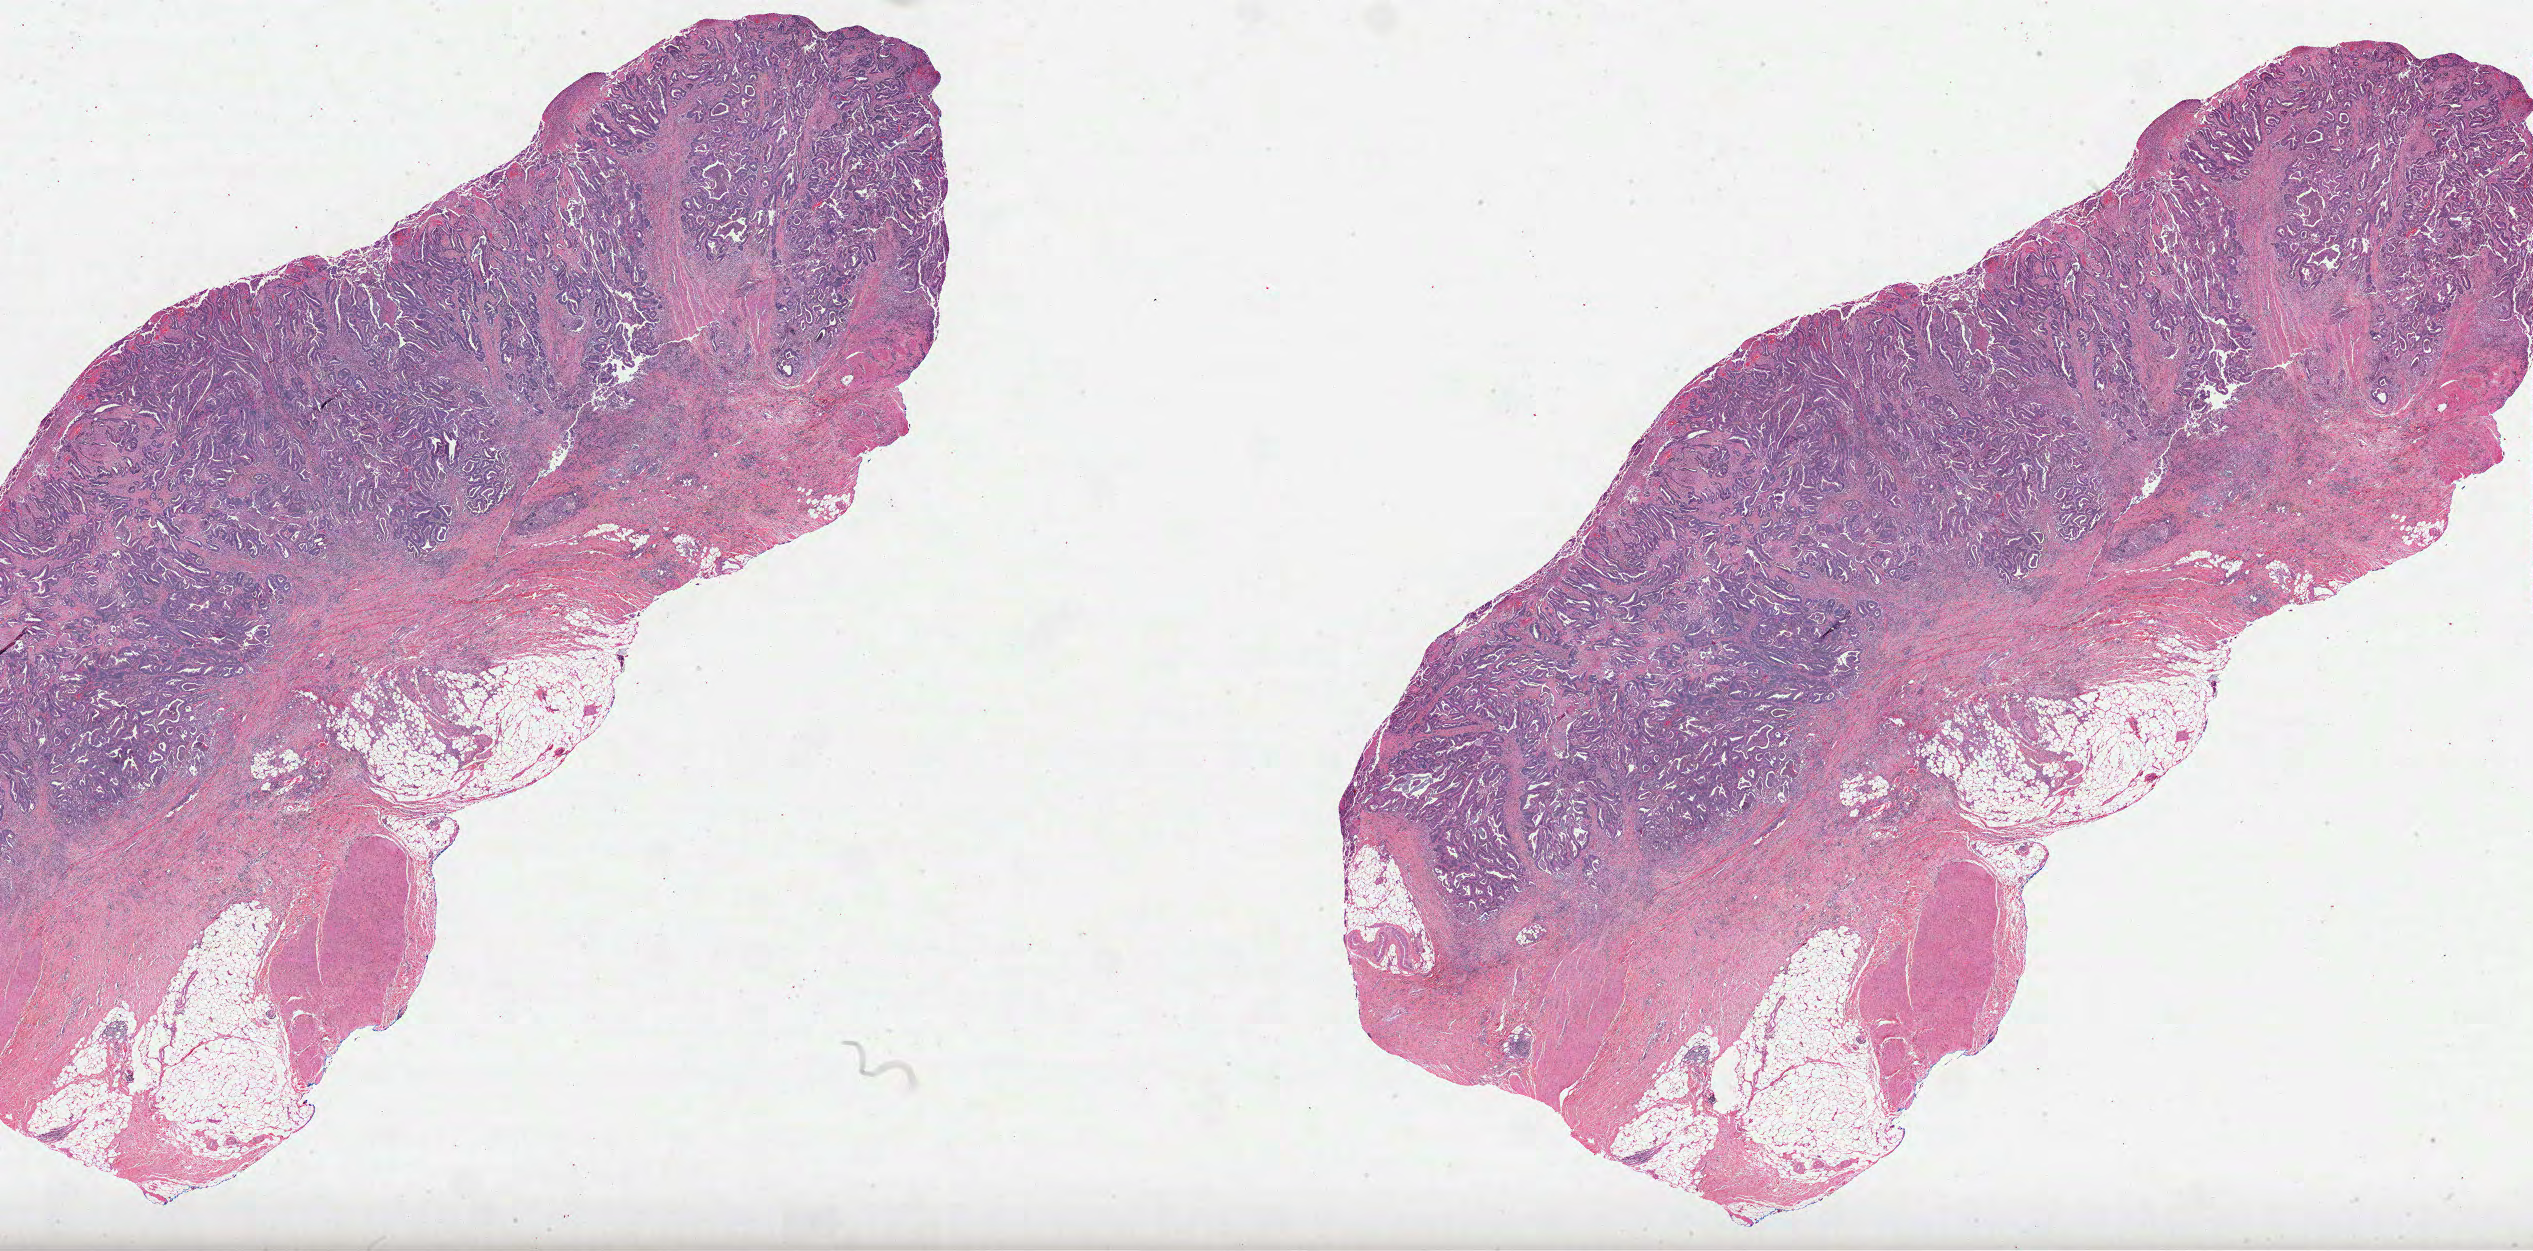
H&E-stained whole-slide image — shown as a low-resolution overview of the whole scanned area (about 40.9 x 20.2 mm, slide scanned at 40x), FFPE section, primary tumour sample from the rectum. Male patient; age at initial diagnosis 73 years.
AJCC pathologic stage: IIIB. Pathologic diagnosis: Adenocarcinoma, NOS.